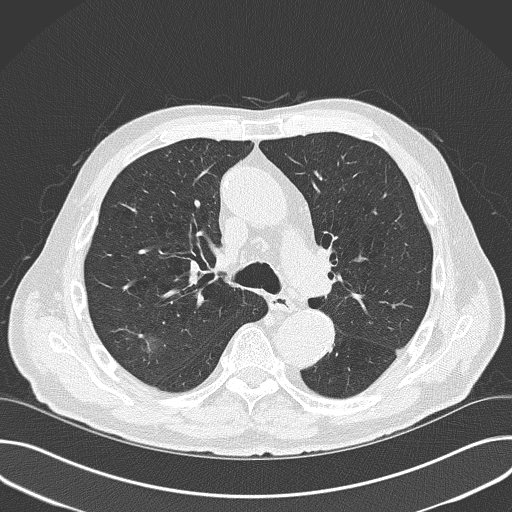
Low-dose screening chest CT, one axial slice. 120 kVp. Lung window (W 1500 / L -600 HU). 2 mm slice thickness. 512 × 512 image matrix, field of view 380 × 380 mm.
Structures marked on this image (outlined manually by an expert reader):
- lesion 1 (tumor, upper lobe of right lung): bounding box <146,334,161,351> (left, top, right, bottom; pixels)